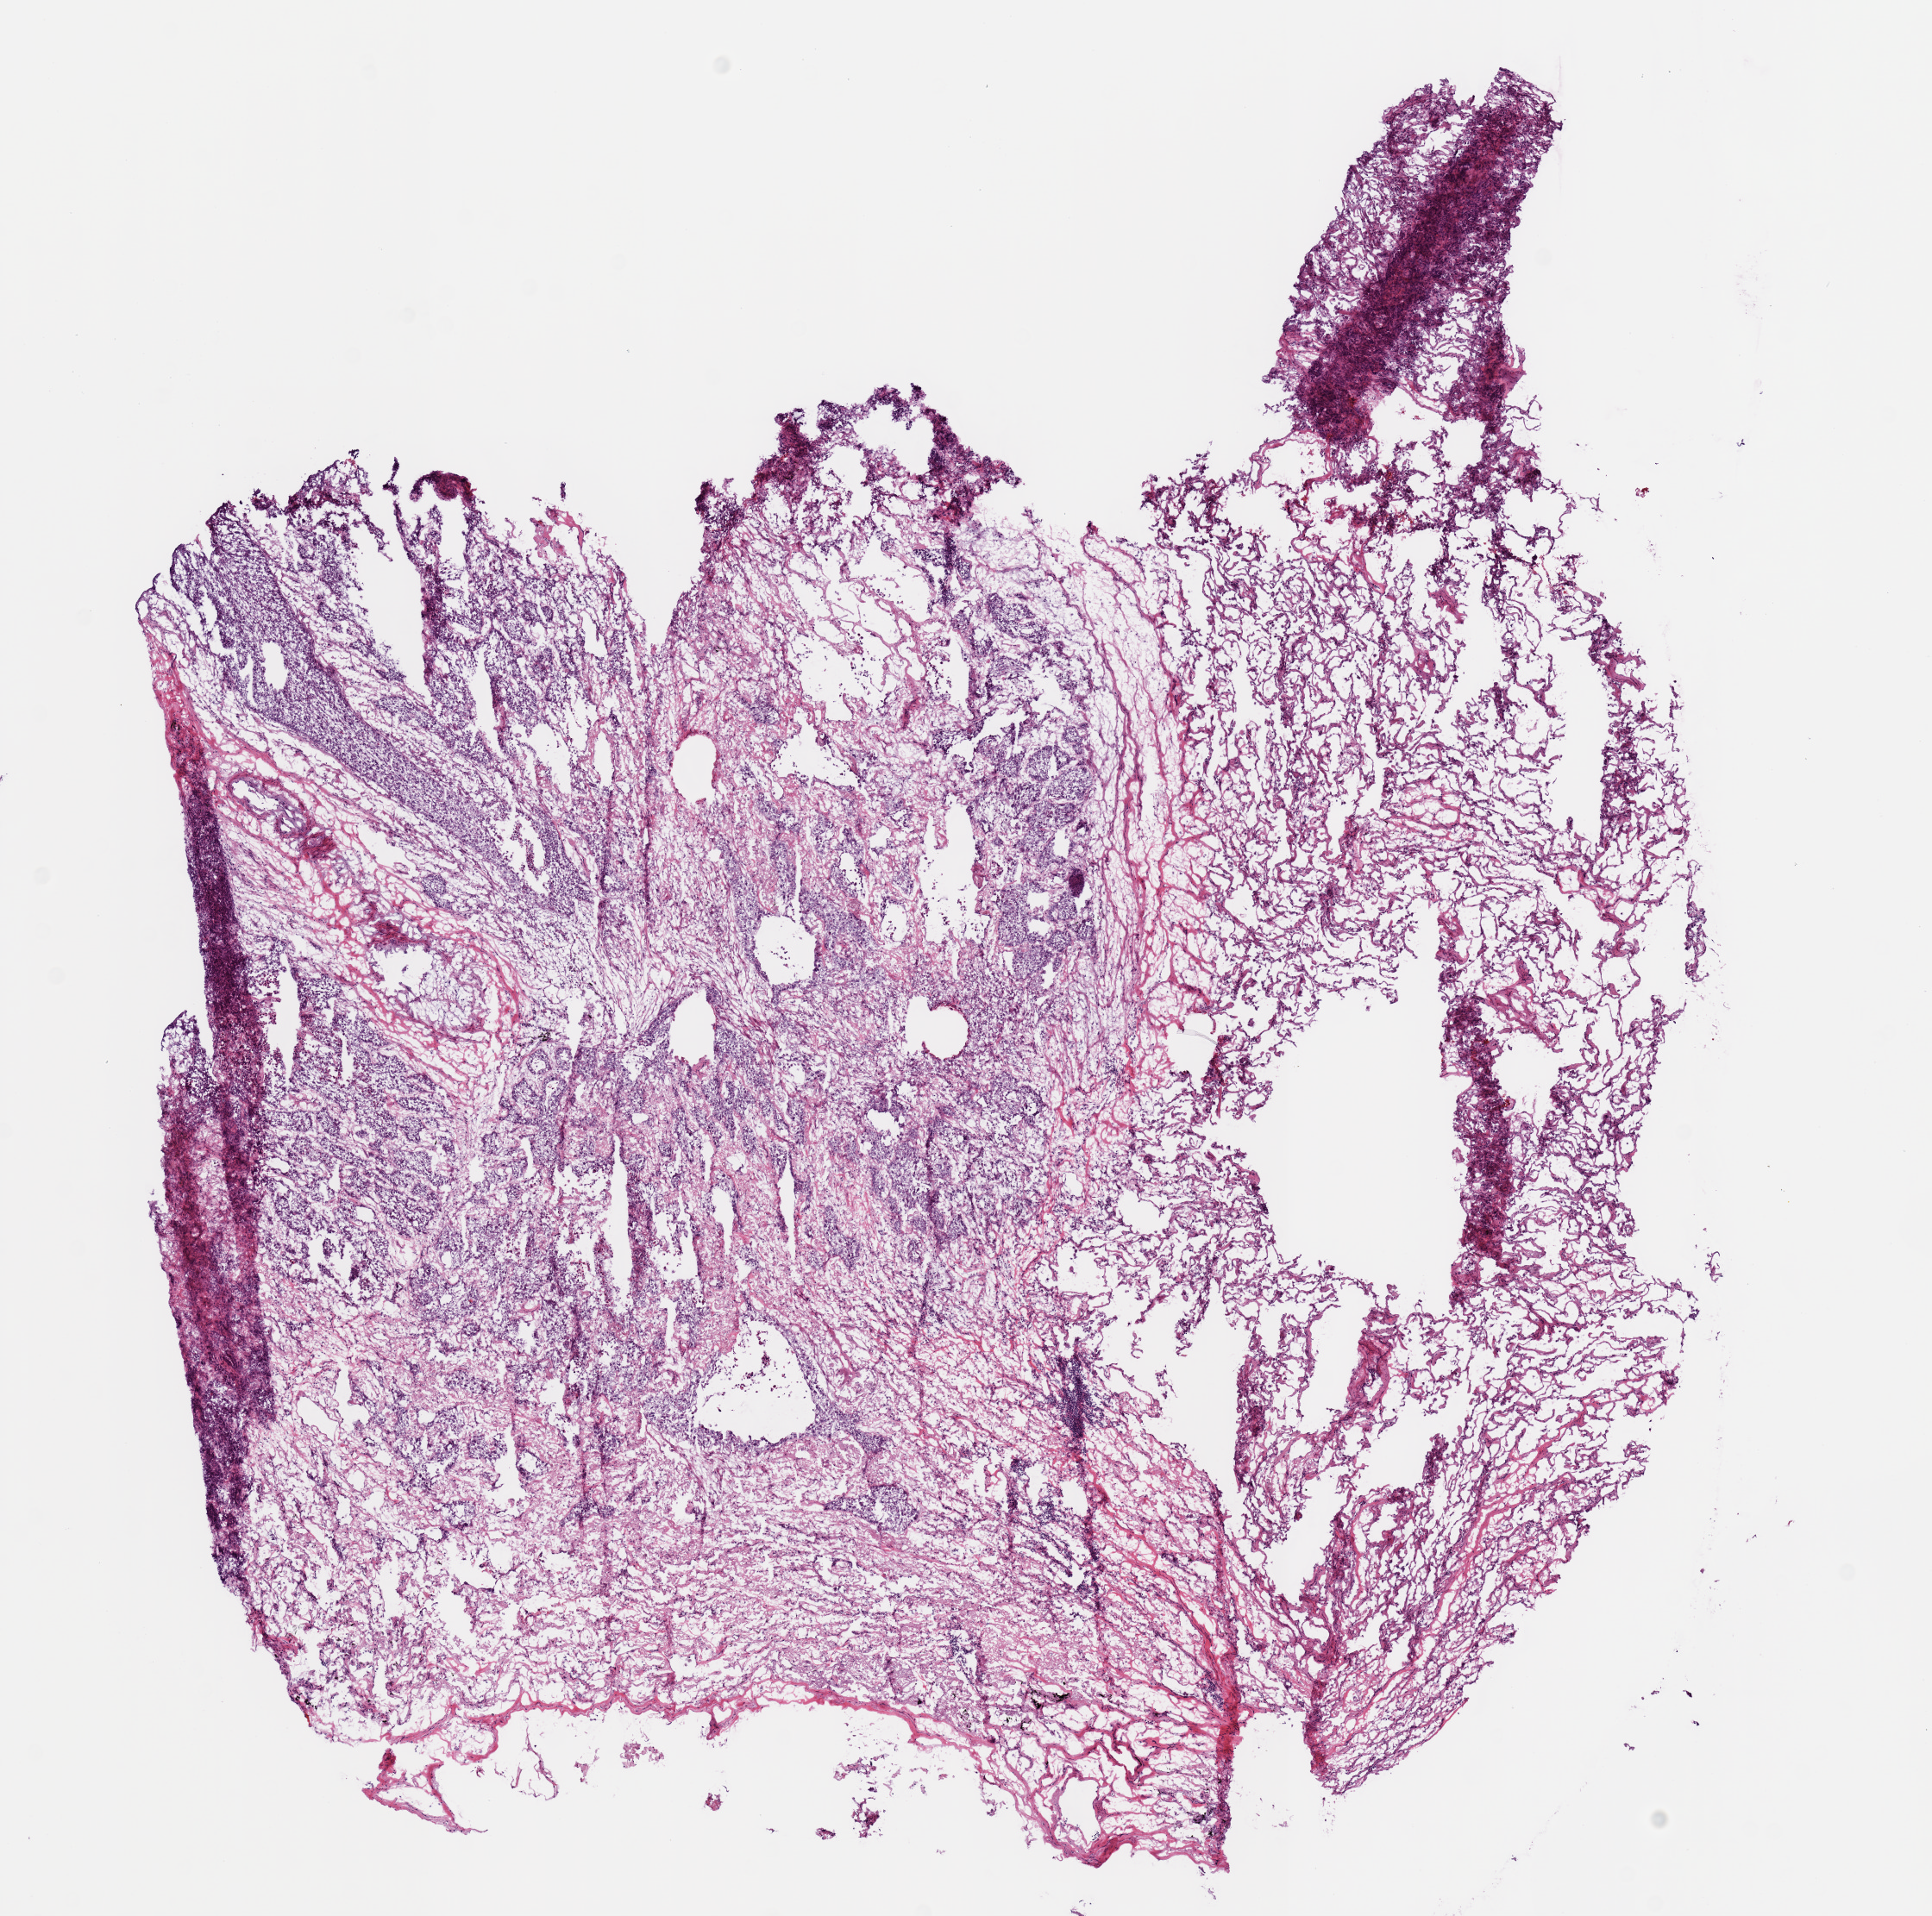
Whole-slide histology image, H&E — shown as a low-resolution overview of the whole scanned area (about 8.9 x 8.8 mm, slide scanned at 20x). Frozen section from the top of the tissue portion. Lung, primary tumour sample. Patient: male, age at initial diagnosis 71 years. Pathologist review of this section (percent, as recorded): tumour nuclei 70%, necrosis 0%.
- AJCC pathologic stage: IB
- pathologic diagnosis: Squamous cell carcinoma, NOS (upper lobe, lung)
- TNM: T2a N0 MX
- laterality: right